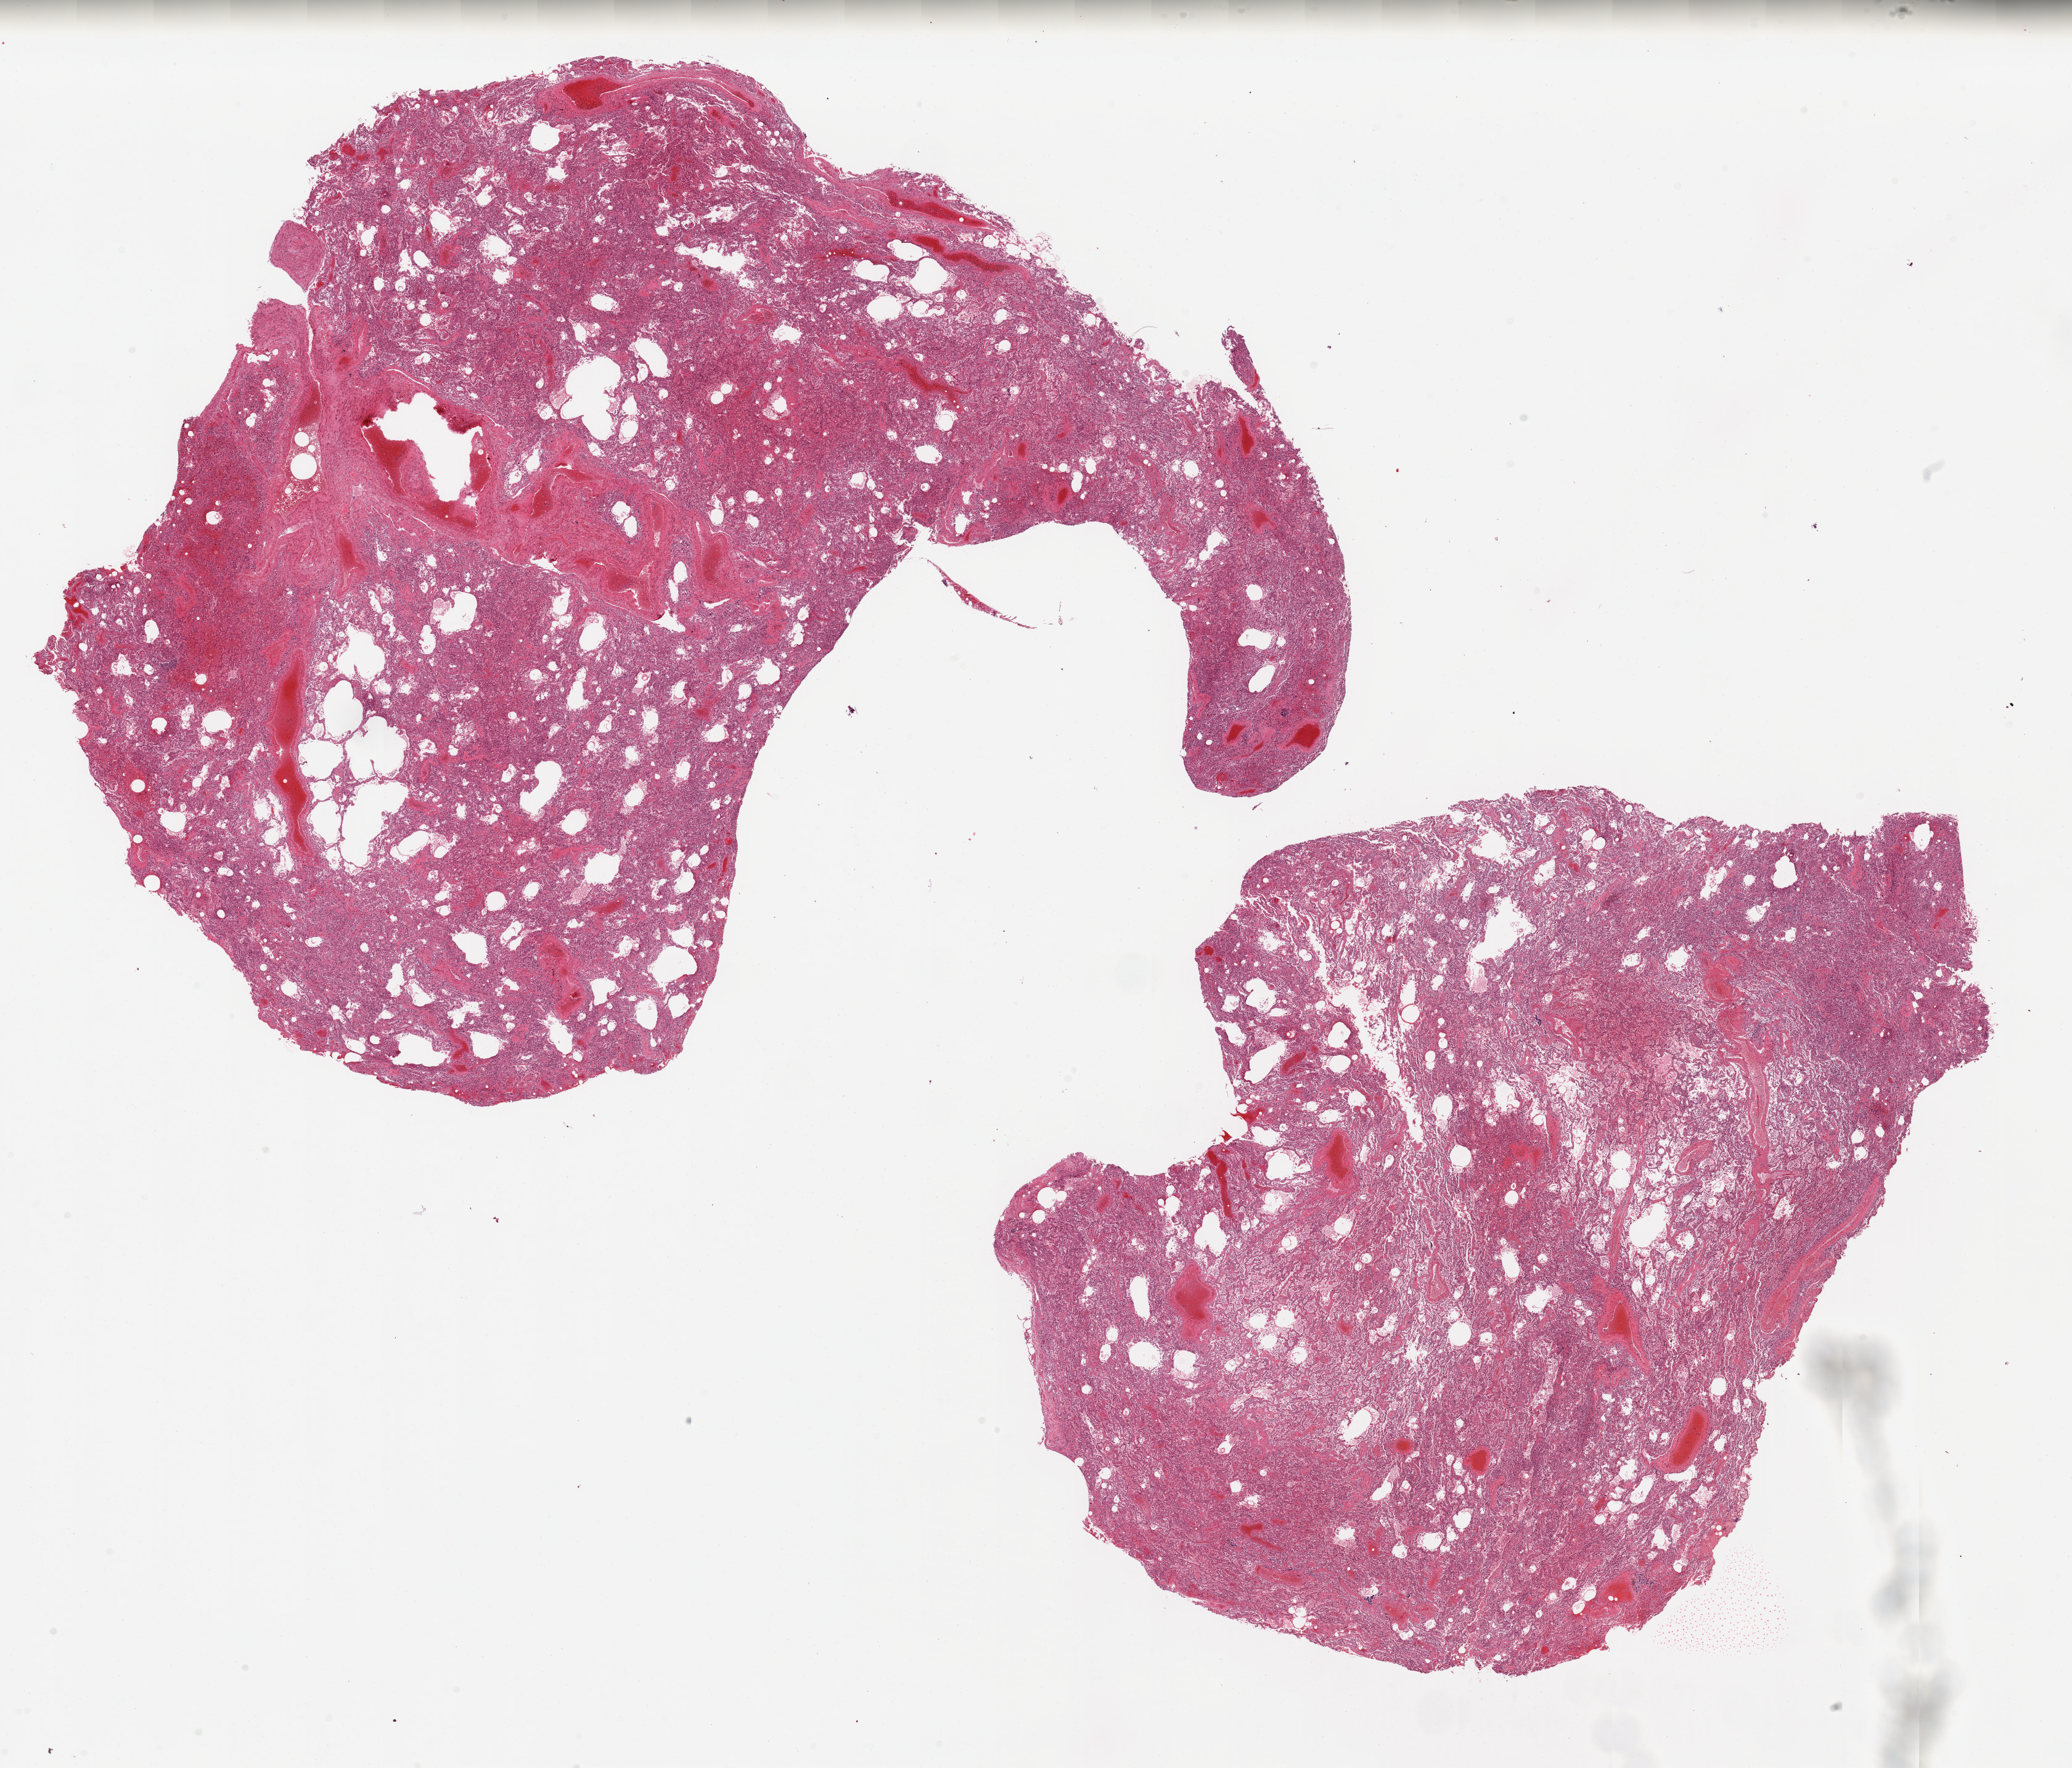
Whole-slide image, haematoxylin and eosin stain — shown as a low-resolution overview of the whole scanned area (about 26.6 x 22.7 mm, slide scanned at 20x), PAXgene-fixed, paraffin-embedded tissue, sampled site (target tissue): lung, tissue donor sample. Donor: male.
Review note (as recorded): 2 pieces, diffuse severe congestion, chronic, with superimosed acute pneumonitis/pneumonia.